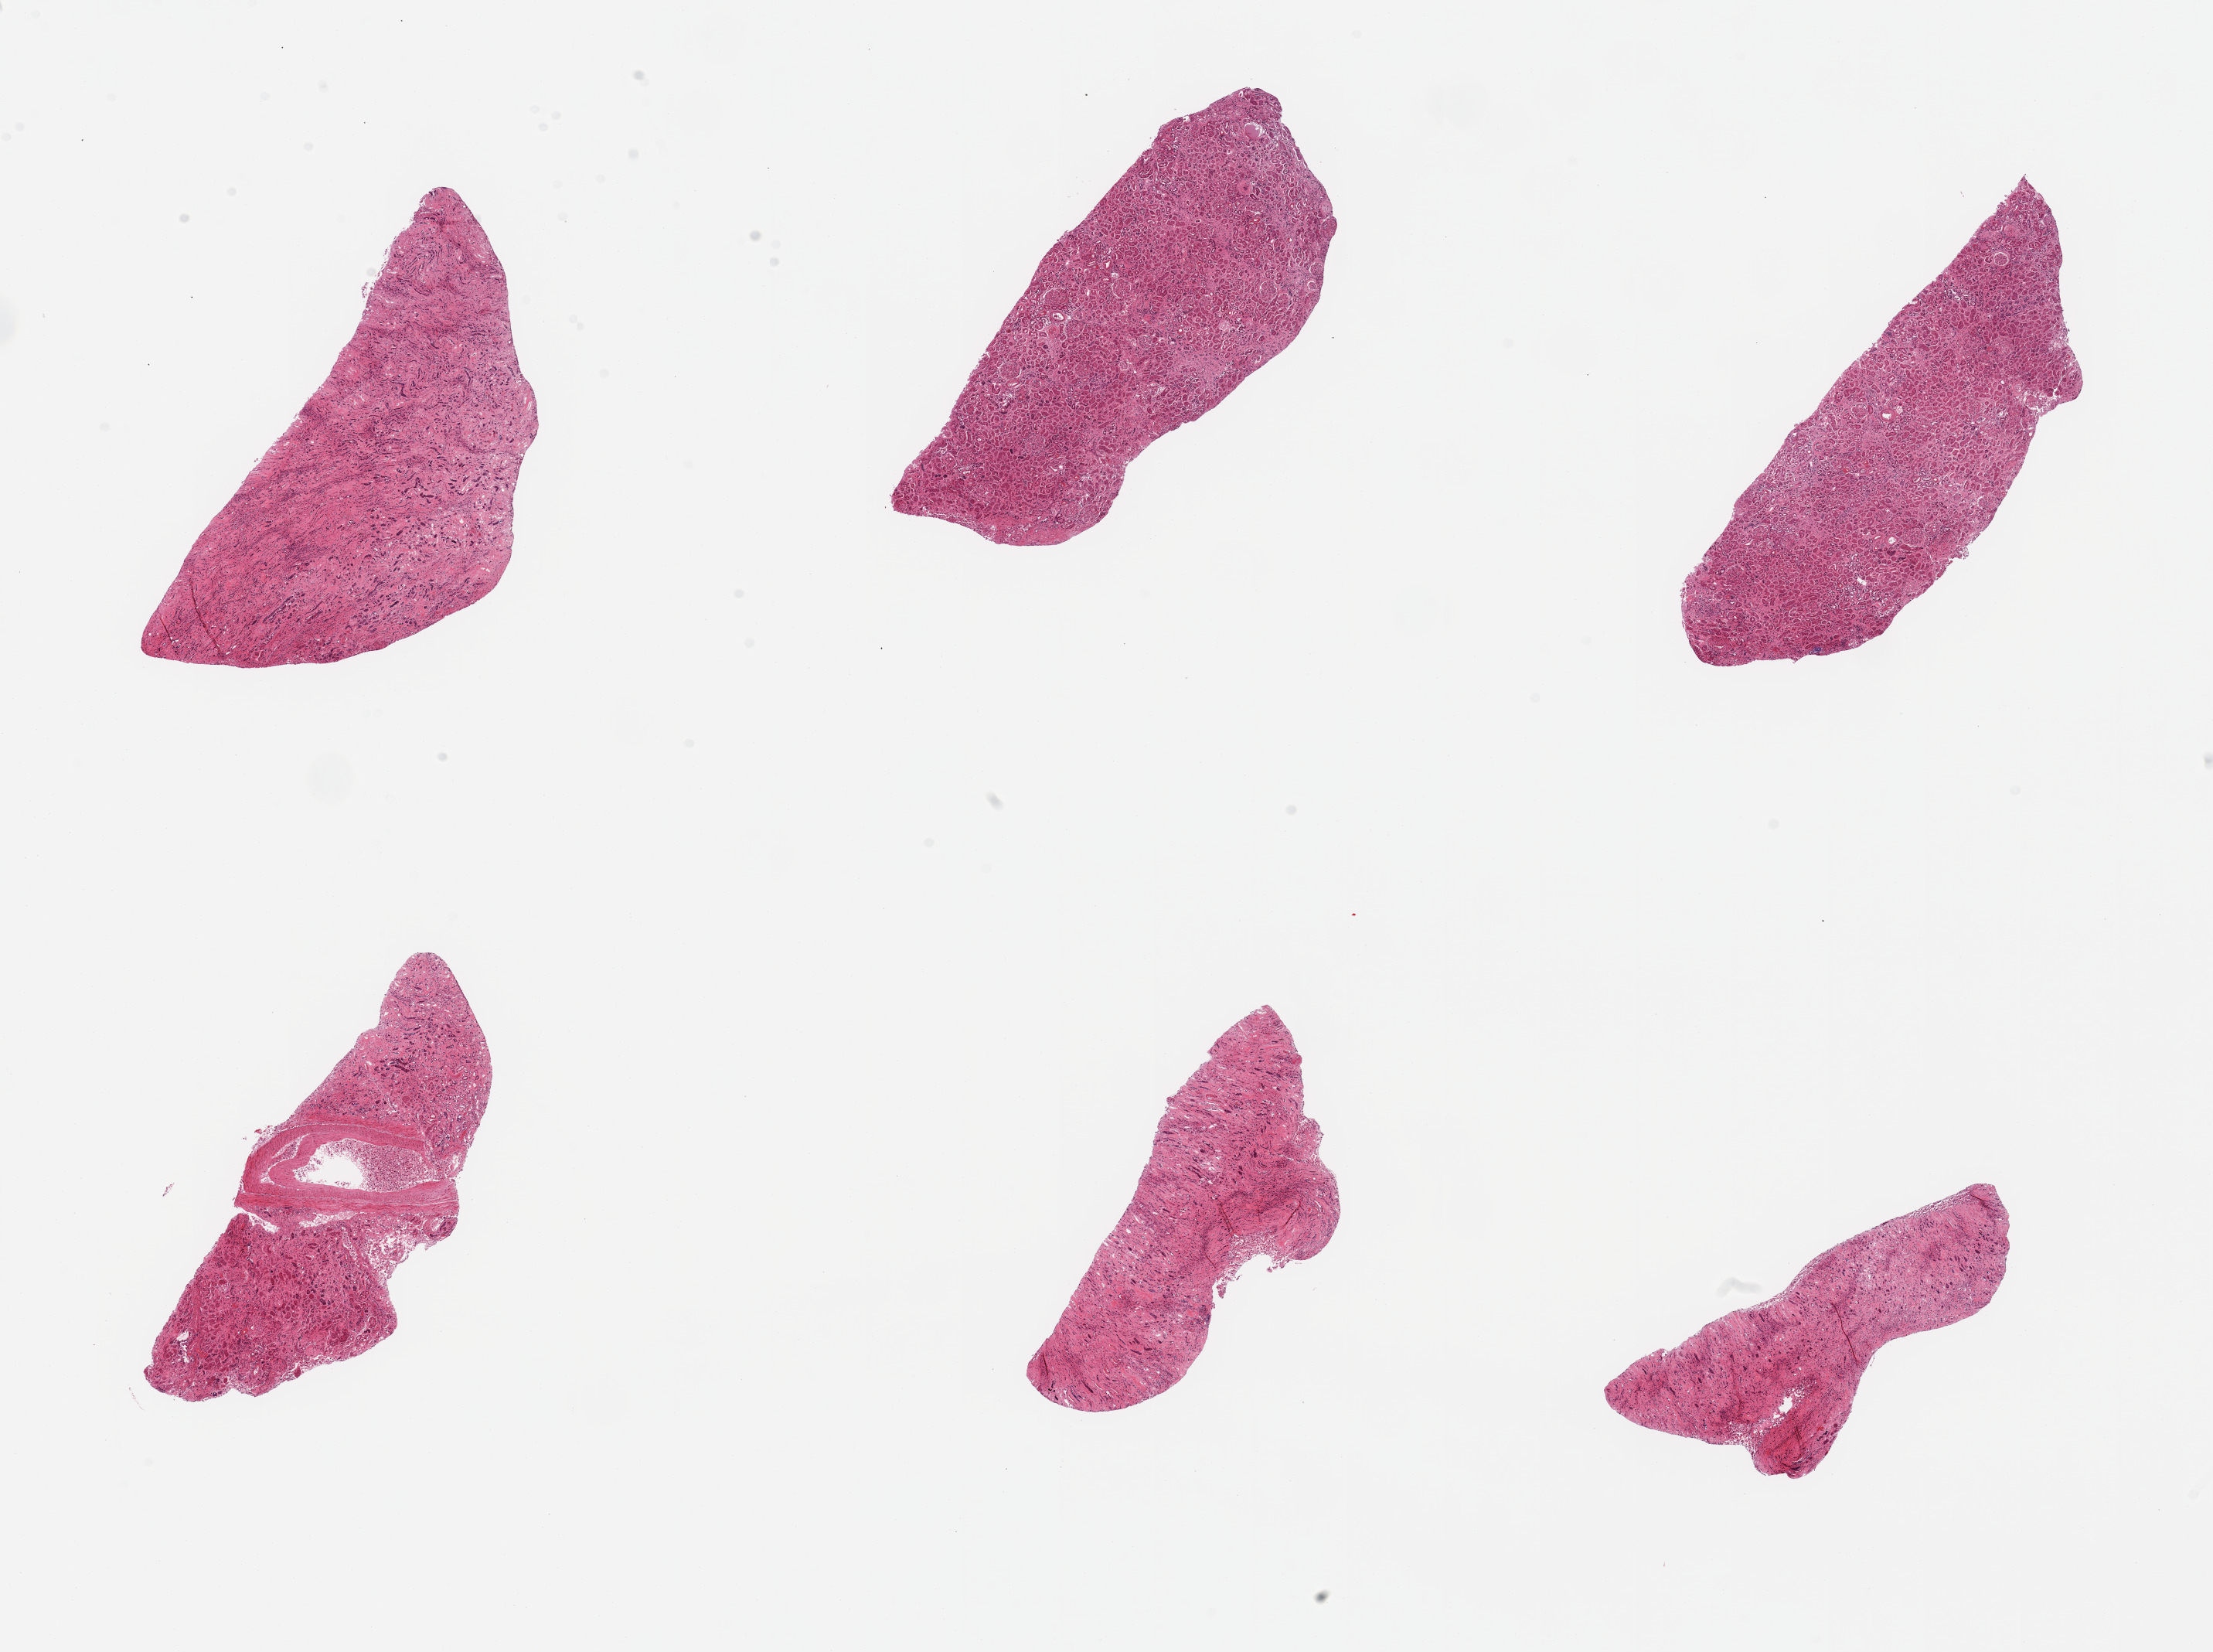
Hematoxylin and eosin (H&E) whole-slide image — a low-resolution overview of the entire scanned area, about 22.6 x 16.9 mm; PAXgene-fixed, paraffin-embedded tissue; section of renal cortex (target tissue); donor tissue sample. Donor: male.
- reviewer comment on this tissue sample: 6 pieces; 2 and 1/2 pieces are cortex, 3 and 1/2 are medulla; extensive arteriolar and glomerular sclerosis